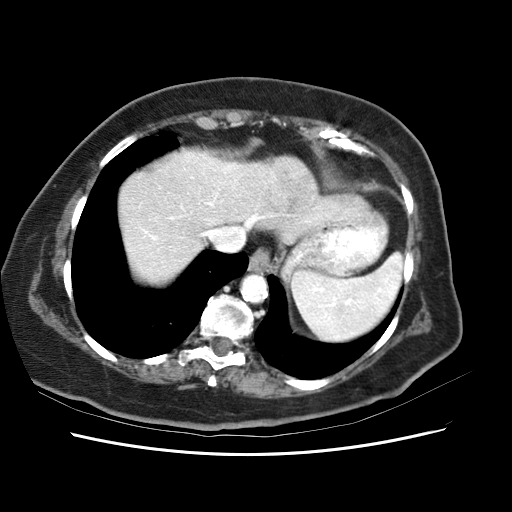
Contrast-enhanced abdominal CT (liver protocol), one axial slice; slice 54 of 62 in the series (ordered by position); reconstruction kernel STANDARD; 120 kVp; soft-tissue window (W 400 / L 40 HU); 512 × 512 image matrix, field of view 340 × 340 mm. From the clinical record (not read from this slice): diagnosis: hepatocellular carcinoma (patient treated with transarterial chemoembolisation; whether this scan precedes or follows treatment is not stated here); TNM stage (as recorded): Stage-I; Child-Pugh class: B; tumour nodularity: uninodular; tumour size: 5.3 cm.
Outlined on this slice (semi-automatically segmented with operator editing):
- abdominal aorta: bounding box <242,275,266,303> (left, top, right, bottom; pixels)
- liver parenchyma outside the tumour (the mass and vessels are separate outlines, so this box may not span the whole liver): <124,152,272,262>
- mass: <269,158,314,208>